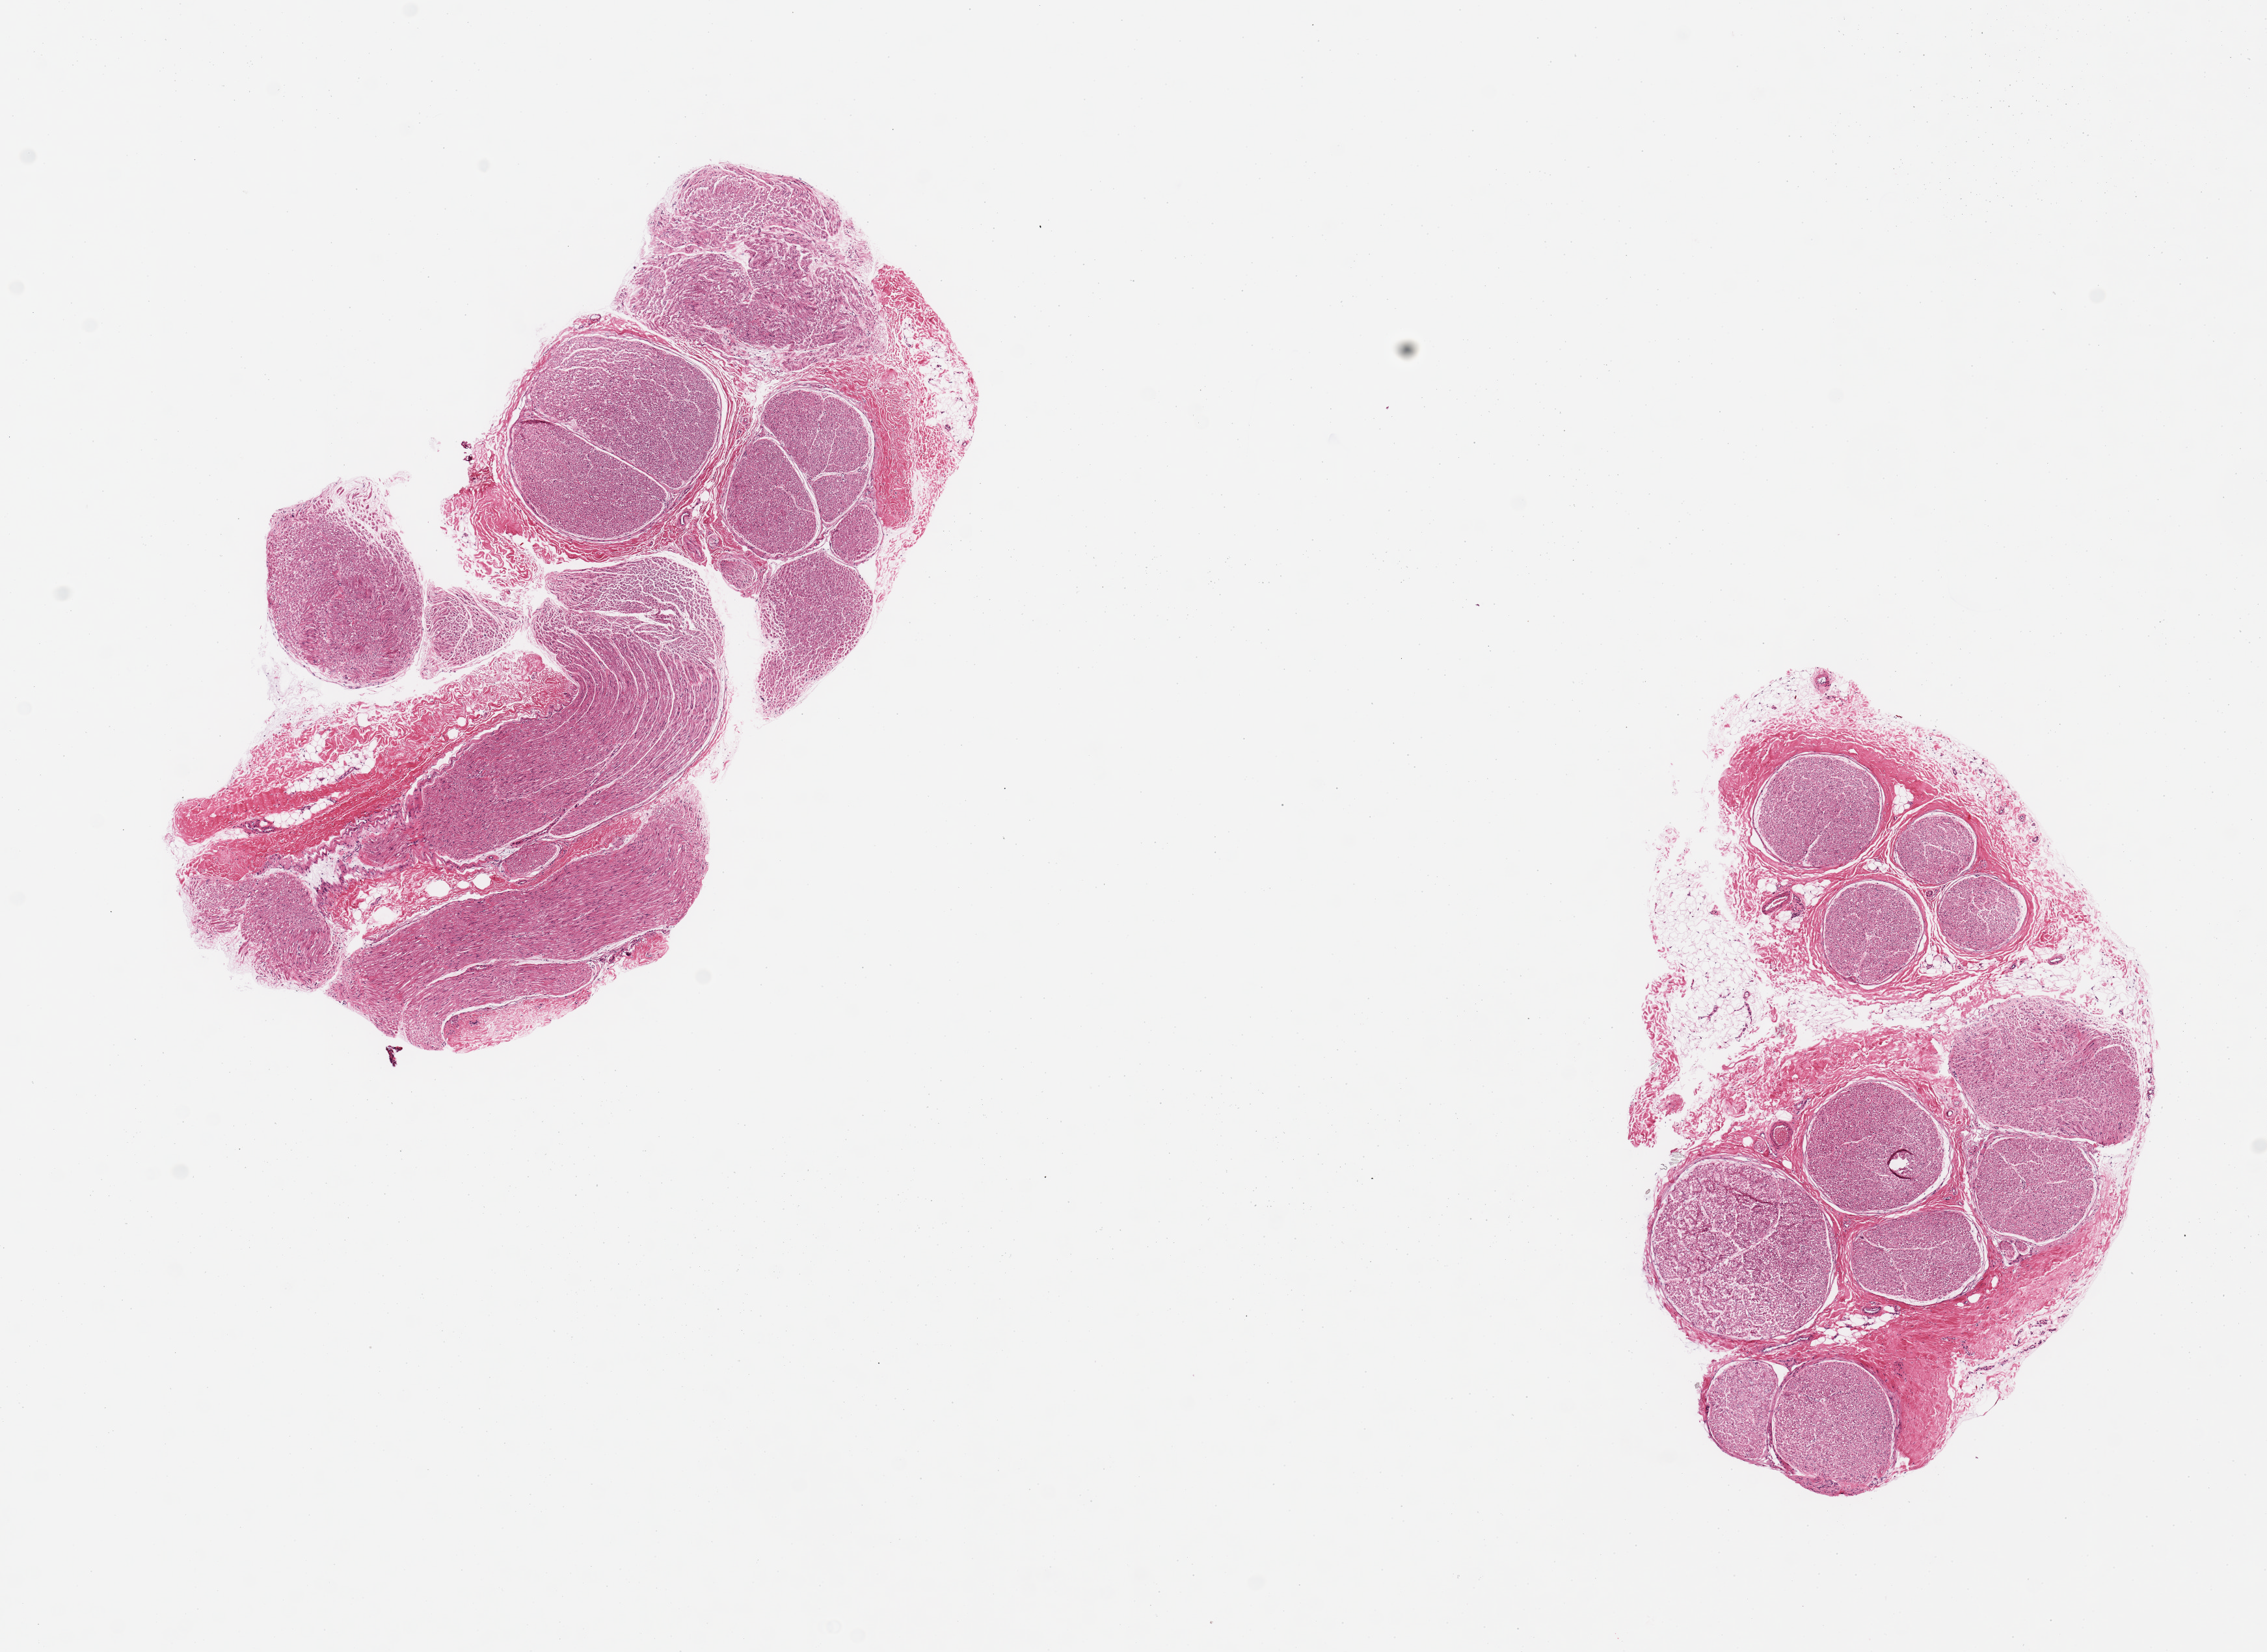
Digitized H&E-stained section — whole scanned area (about 13.8 x 10.0 mm) shown as a low-resolution overview, PAXgene-fixed paraffin-embedded (PFPE) section, target tissue: tibial nerve, tissue donor sample.
• reviewer comment on this tissue sample: 2 pieces, trace adherent fat